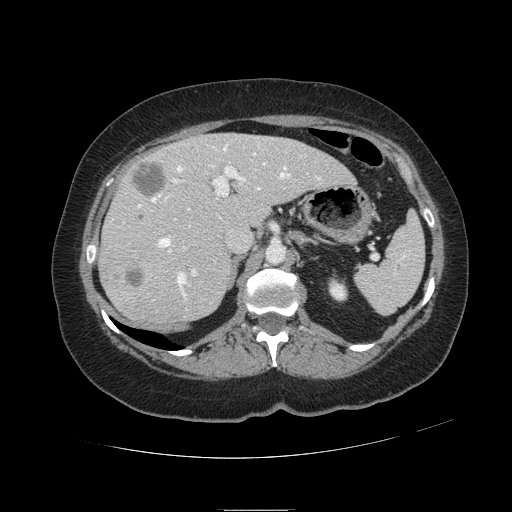
Contrast-enhanced abdominal CT, one axial slice. Slice 69 of 121 in the series (ordered by position). 120 kVp. Intravenous contrast given. Soft-tissue window (W 400 / L 40 HU). 512 × 512 image matrix, field of view 400 × 400 mm. Female patient, age 52 years. Case-level facts recorded for this patient, not image findings: diagnosis: colorectal cancer liver metastases, imaged before liver resection; multiple liver metastases: yes; largest metastasis: 6.3 cm.
Annotated regions visible in this slice (outlined manually by an expert reader):
- hepatic veins: bounding box <138,144,321,298> (left, top, right, bottom; pixels)
- liver: <100,134,353,322>
- planned liver remnant (the part of the liver to remain after resection): <167,134,353,226>
- portal vein (with intrahepatic branches): <172,162,266,275>
- liver metastasis: <130,161,167,196>
- liver metastasis: <126,268,143,288>